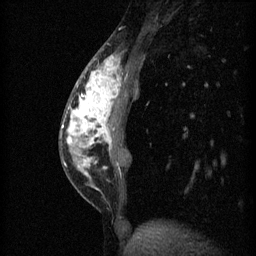
Breast MRI (dynamic contrast-enhanced), one sagittal slice. Slice 18 of 60 in the series (ordered by position). 3 images stored at this slice position (order not interpretable as contrast timing). 1.5 T. TE 4.2 ms, TR 11 ms. 256 × 256 image matrix. Patient: female, 40 years.
Annotated regions visible in this slice (semi-automatically segmented with operator editing):
- analysis volume of interest (the breast-tissue region the enhancement analysis was run in; not a lesion): bounding box <61,44,137,203> (left, top, right, bottom; pixels)
- tumour enhancement mask (voxels above the 70 % enhancement threshold inside the analysis volume of interest): <63,56,122,191>